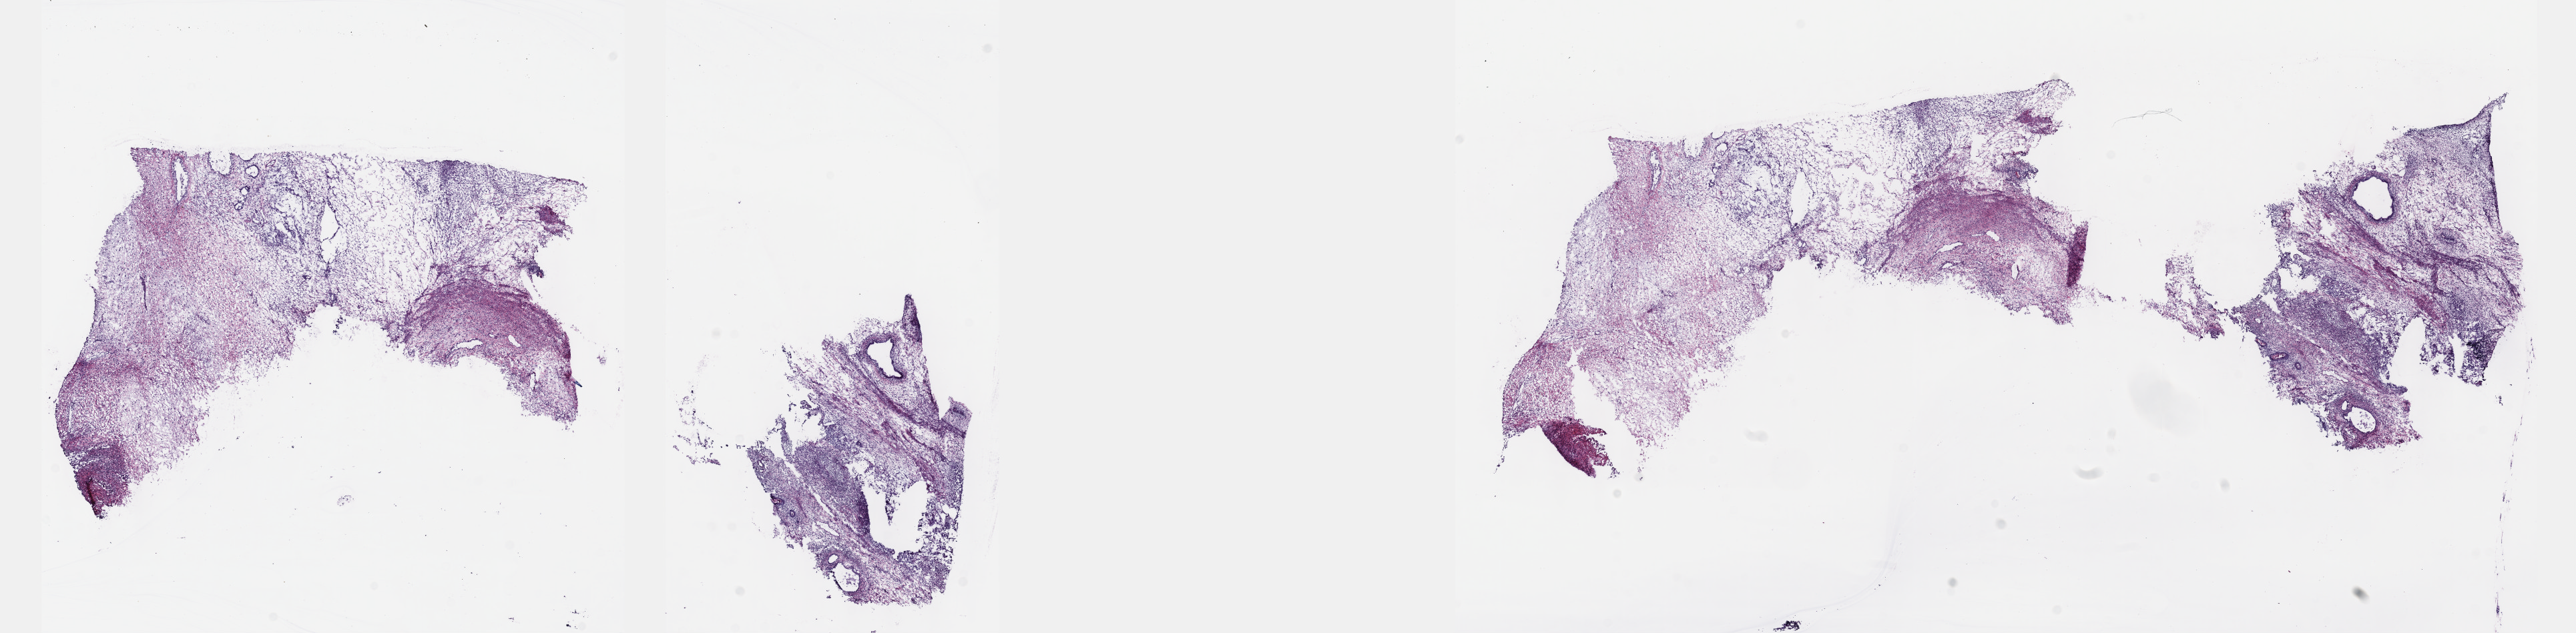
Whole-slide histology image, H&E, a low-resolution overview of the entire scanned area, about 31.2 x 7.7 mm (from a 40x scan). Patient sex: male. Pathologist review of this section (percent, as recorded): tumour cells 60%, tumour nuclei 60%, normal cells 0%, stromal cells 40%, necrosis 0%. Infiltration values recorded for this section: lymphocyte infiltration 40%, monocyte infiltration 20%, neutrophil infiltration 20%.
Specimen: frozen section from the top of the tissue portion; testis, primary tumour sample.